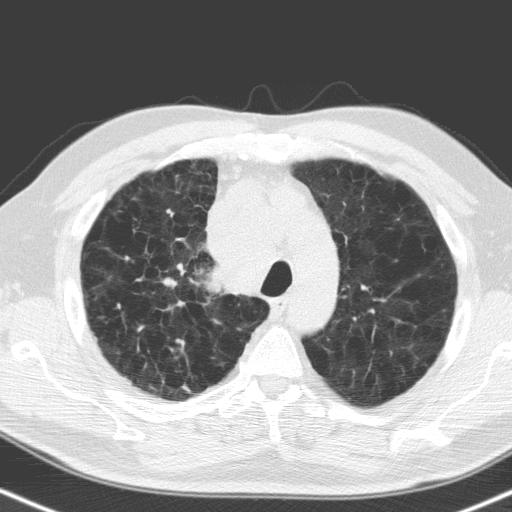
Low-dose screening chest CT, one axial slice; position 127 of 160 along the scan axis; 120 kVp; lung window (W 1500 / L -600 HU); 512 × 512 image matrix, field of view 324 × 324 mm.
Outlined on this slice (expert manual segmentation):
- lesion 1 (tumor, hilum of right lung): box from (x=209, y=264) to (x=245, y=293) px